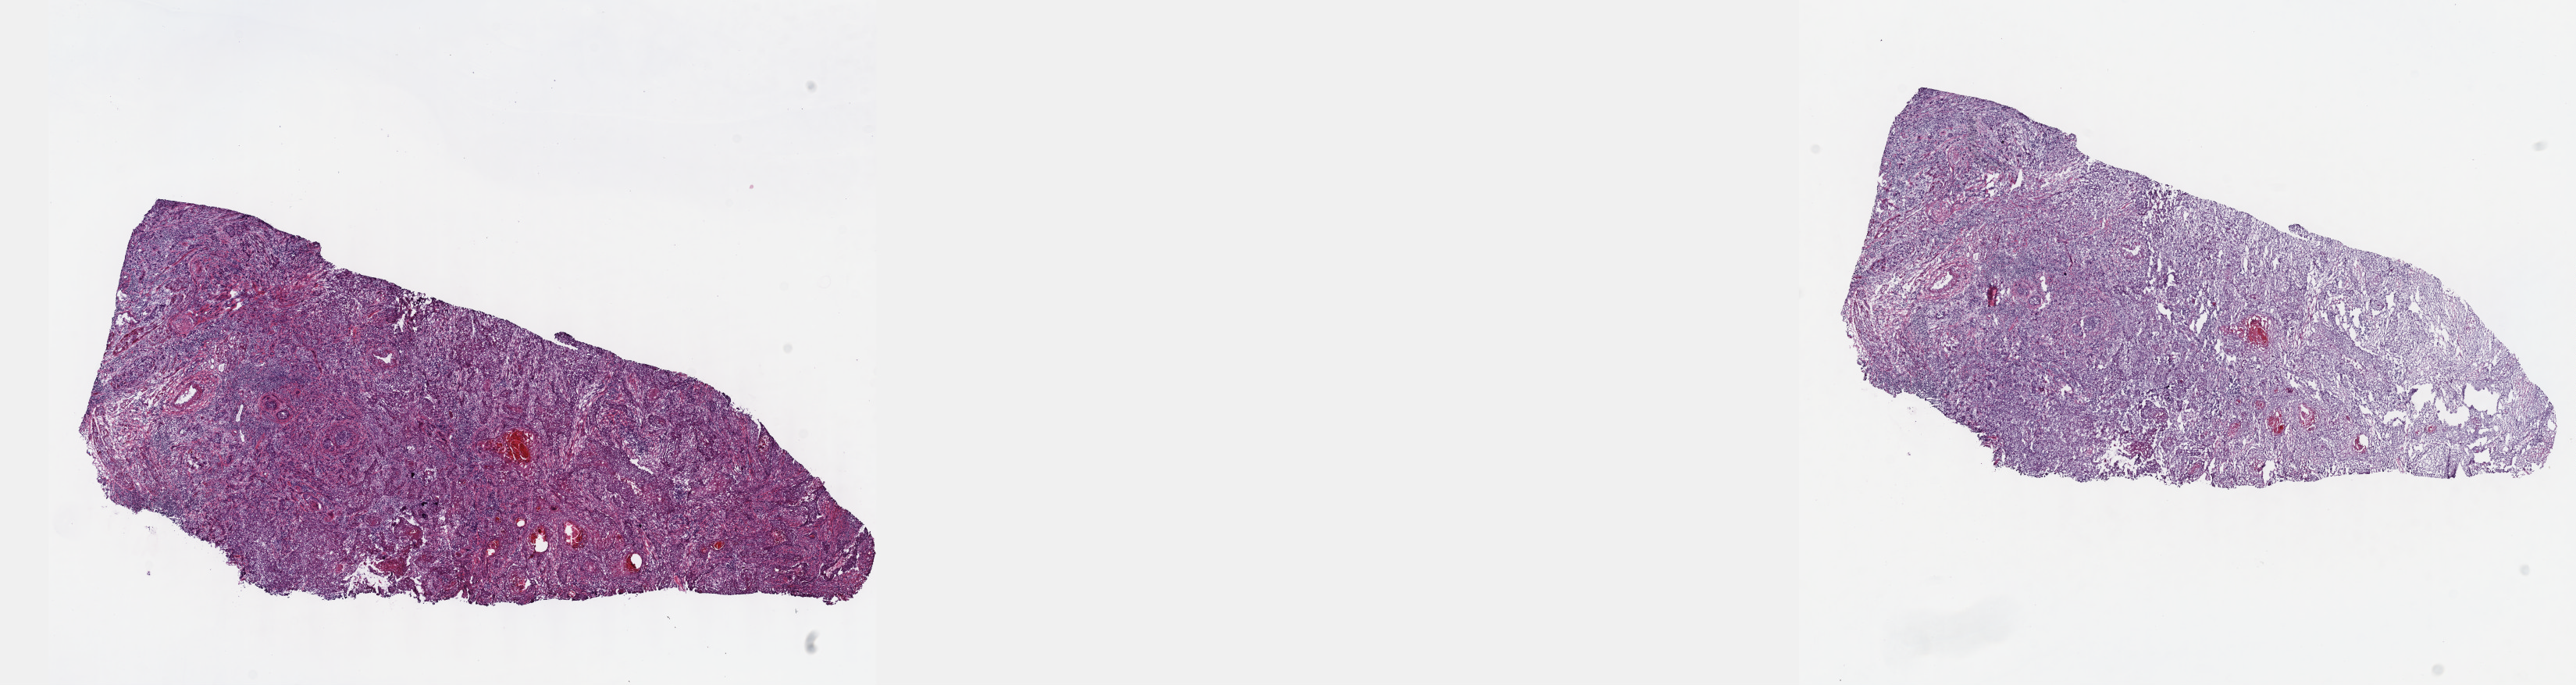
H&E-stained whole-slide image — low-resolution overview of the scanned area, about 26.7 x 7.1 mm (slide scanned at 40x); frozen section from the top of the tissue portion; head and neck, primary tumour sample. Patient: male, age at initial diagnosis 66 years. Histologic grade: G2 (moderately differentiated). Composition of this section per pathologist review: tumour cells 60%, tumour nuclei 70%, normal cells 0%, stromal cells 40%, necrosis 0%. Infiltration values recorded for this section: lymphocyte infiltration 10%, monocyte infiltration 0%, neutrophil infiltration 0%.
Pathologic diagnosis: Squamous cell carcinoma, keratinizing, NOS (tongue, NOS). Lymph nodes positive (case pathology): 6 of 44 examined. AJCC pathologic stage: IVA. Laterality: right.